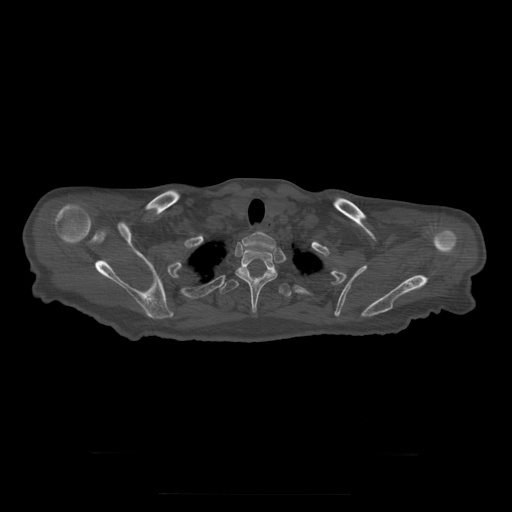
CT including the spine, one axial slice; reconstruction kernel STANDARD; 120 kVp; bone window (W 1800 / L 400 HU); 1.25 mm slice thickness; 512 × 512 image matrix, field of view 510 × 510 mm. Patient age 73 years. Case-level facts recorded for this patient, not image findings: primary cancer: prostate.
Outlined on this slice (semi-automatically segmented with operator editing):
- T1 vertebra: box from (x=242, y=231) to (x=276, y=250) px
- T2 vertebra: (x=235, y=250)–(x=278, y=313)
- T3 vertebra: (x=220, y=268)–(x=292, y=297)